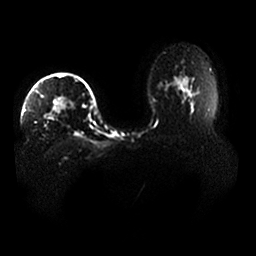
Breast MRI, one axial slice. Position 30 of 33 along the scan axis. Diffusion-weighted series; image 2 of 4 stored at this slice position (different b-values; order by instance number). 1.5 T. 256 × 256 image matrix, field of view 400 × 400 mm. Female patient.
Outlined on this slice (manually delineated by an expert):
- tumour on diffusion-weighted imaging: bounding box [x1, y1, x2, y2] px = [47, 99, 69, 119]